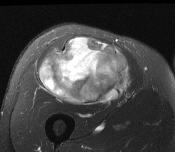
MRI of an extremity soft-tissue mass, one axial slice; slice 87 of 116 in the series (ordered by position); T2-weighted fat-saturated; MR volume resampled by the dataset authors to the PET/CT grid (not the native acquisition matrix); 3.27 mm slice thickness; 175 × 152 image matrix, field of view 171 × 148 mm. Male patient. From the clinical record (not read from this slice): histological type: pleiomorphic leiomyosarcoma; grade: intermediate; site of the primary tumour: right thigh.
Outlined on this slice (expert contour drawn on MRI and transferred to this co-registered scan by the dataset authors):
- gross tumour volume including surrounding oedema: bounding box (x1, y1, x2, y2) in pixels: (40, 37, 130, 105)
- gross tumour volume (mass): (40, 37, 130, 105)